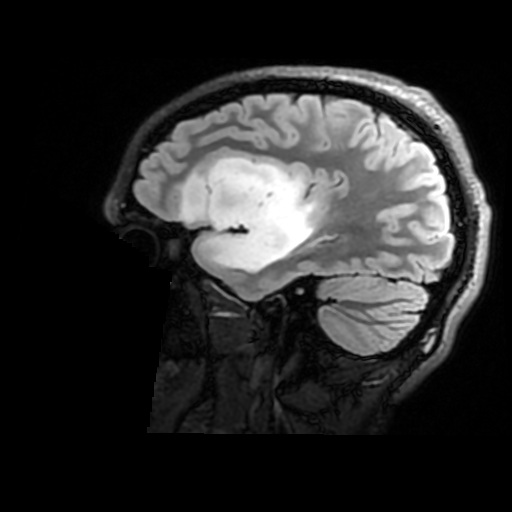
Brain MRI from a brain-tumour surgery series, one sagittal slice; slice 125 of 176 in the series (ordered by position); T2 FLAIR; 1 mm slice thickness; 512 × 512 image matrix, field of view 240 × 240 mm. From the clinical record (not read from this slice): histopathology: Astrocytoma; WHO grade: 2; IDH mutation: yes; tumour location: Right Insular.
Annotated regions visible in this slice (manually delineated by an expert):
- tumour: bounding box (x1, y1, x2, y2) in pixels: (181, 157, 318, 273)